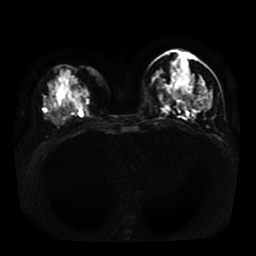
Breast MRI, one axial slice; slice 17 of 41 in the series (ordered by position); diffusion-weighted series; image 2 of 4 stored at this slice position (different b-values; order by instance number); 1.5 T; 5 mm slice thickness; 256 × 256 image matrix, field of view 330 × 330 mm. Female patient.
Outlined on this slice (expert manual segmentation):
- tumour on diffusion-weighted imaging: bounding box [x1, y1, x2, y2] px = [173, 93, 176, 96]